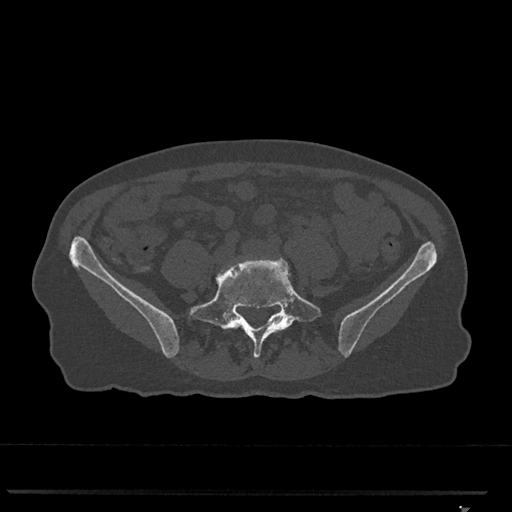
CT including the spine, one axial slice. Slice 158 of 793 in the series (ordered by position). Reconstruction kernel Br40s/3. 120 kVp. Bone window (W 1800 / L 400 HU). 512 × 512 image matrix, field of view 380 × 380 mm. Female patient, age 62 years. Case-level facts recorded for this patient, not image findings: primary cancer: renal.
Annotated regions visible in this slice (semi-automatic segmentation, software-assisted and operator-edited):
- L4 vertebra: box from (x=217, y=259) to (x=259, y=277) px
- L5 vertebra: (x=189, y=258)–(x=321, y=357)